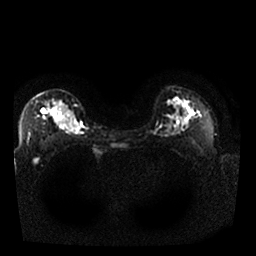
Breast MRI, one axial slice. Position 18 of 25 along the scan axis. Diffusion-weighted series; image 2 of 4 stored at this slice position (different b-values; order by instance number). 1.5 T. 4 mm slice thickness. 256 × 256 image matrix, field of view 340 × 340 mm. Female patient.
Structures marked on this image (expert manual segmentation):
- tumour on diffusion-weighted imaging: bounding box <48,106,72,124> (left, top, right, bottom; pixels)